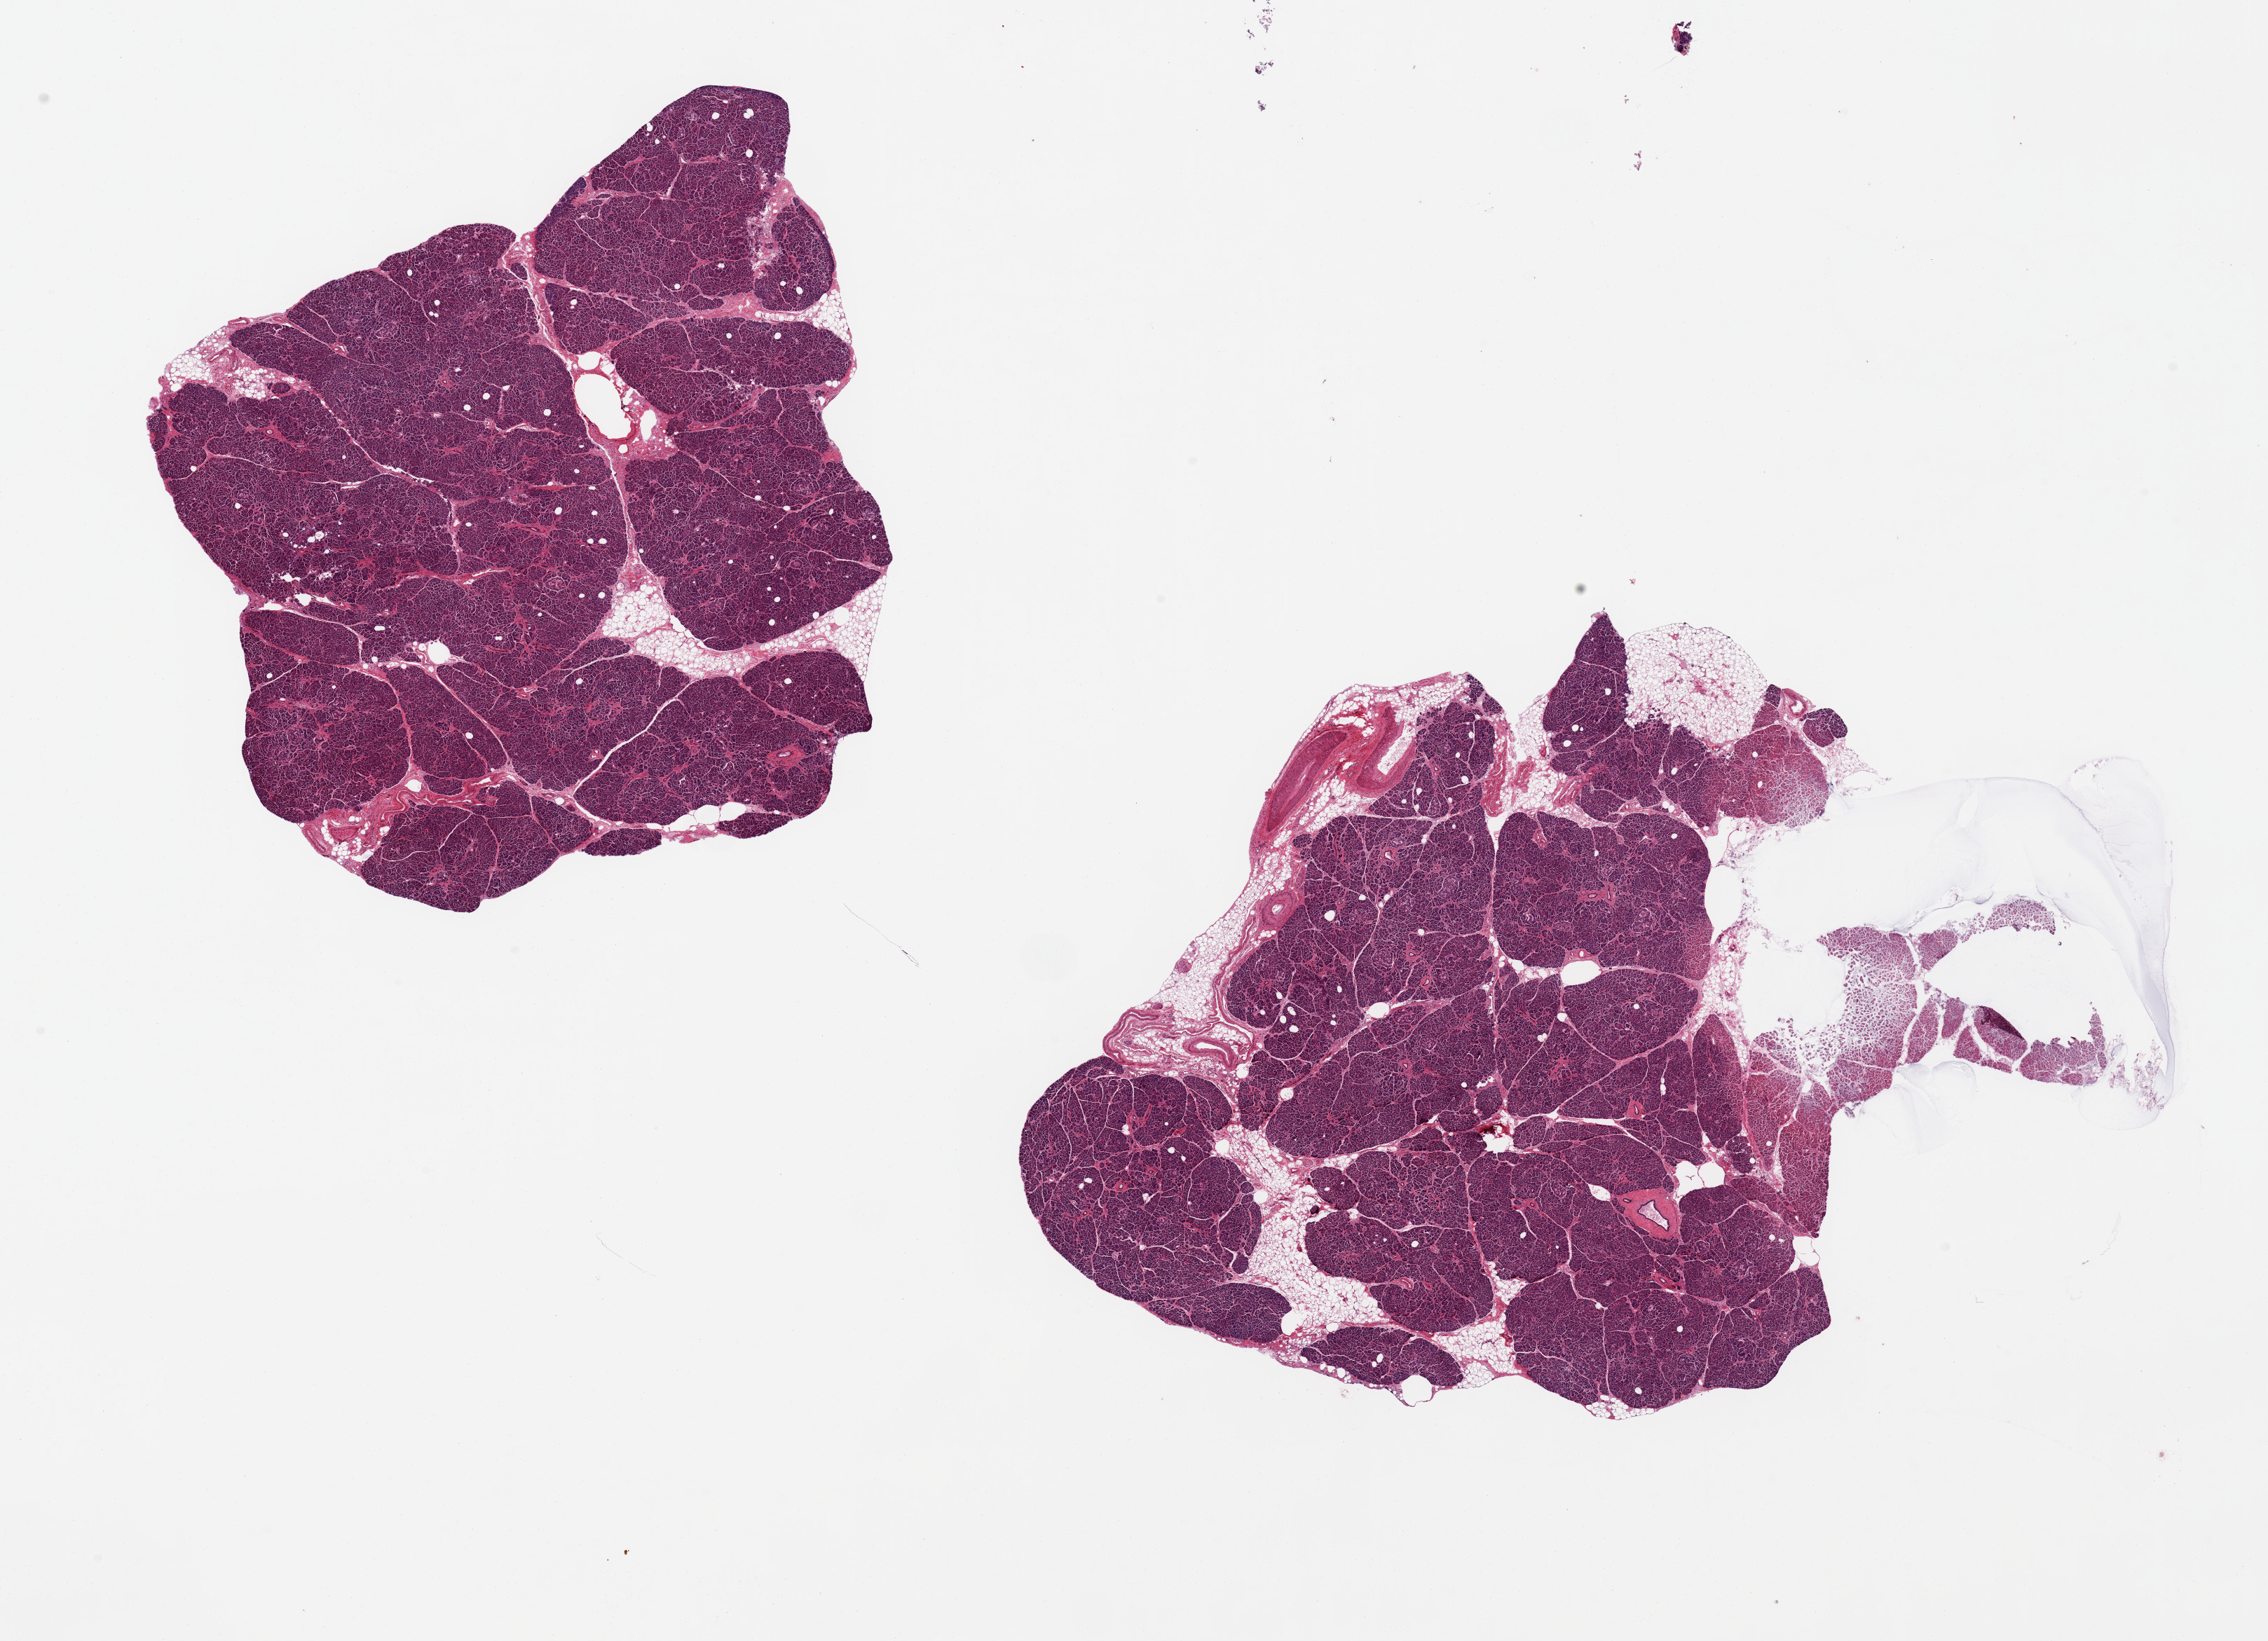
Hematoxylin and eosin (H&E) whole-slide image, shown as a low-resolution overview of the whole scanned area (about 25.6 x 18.5 mm, acquisition: 20x scan). PAXgene-fixed paraffin-embedded (PFPE) section. Section of pancreas (target tissue). Tissue donor sample. Donor sex: female.
Pathologist's review note for this sample: 2 ~ 7x8;9x9 mm pieces, focally autolyzed;<5% fat.